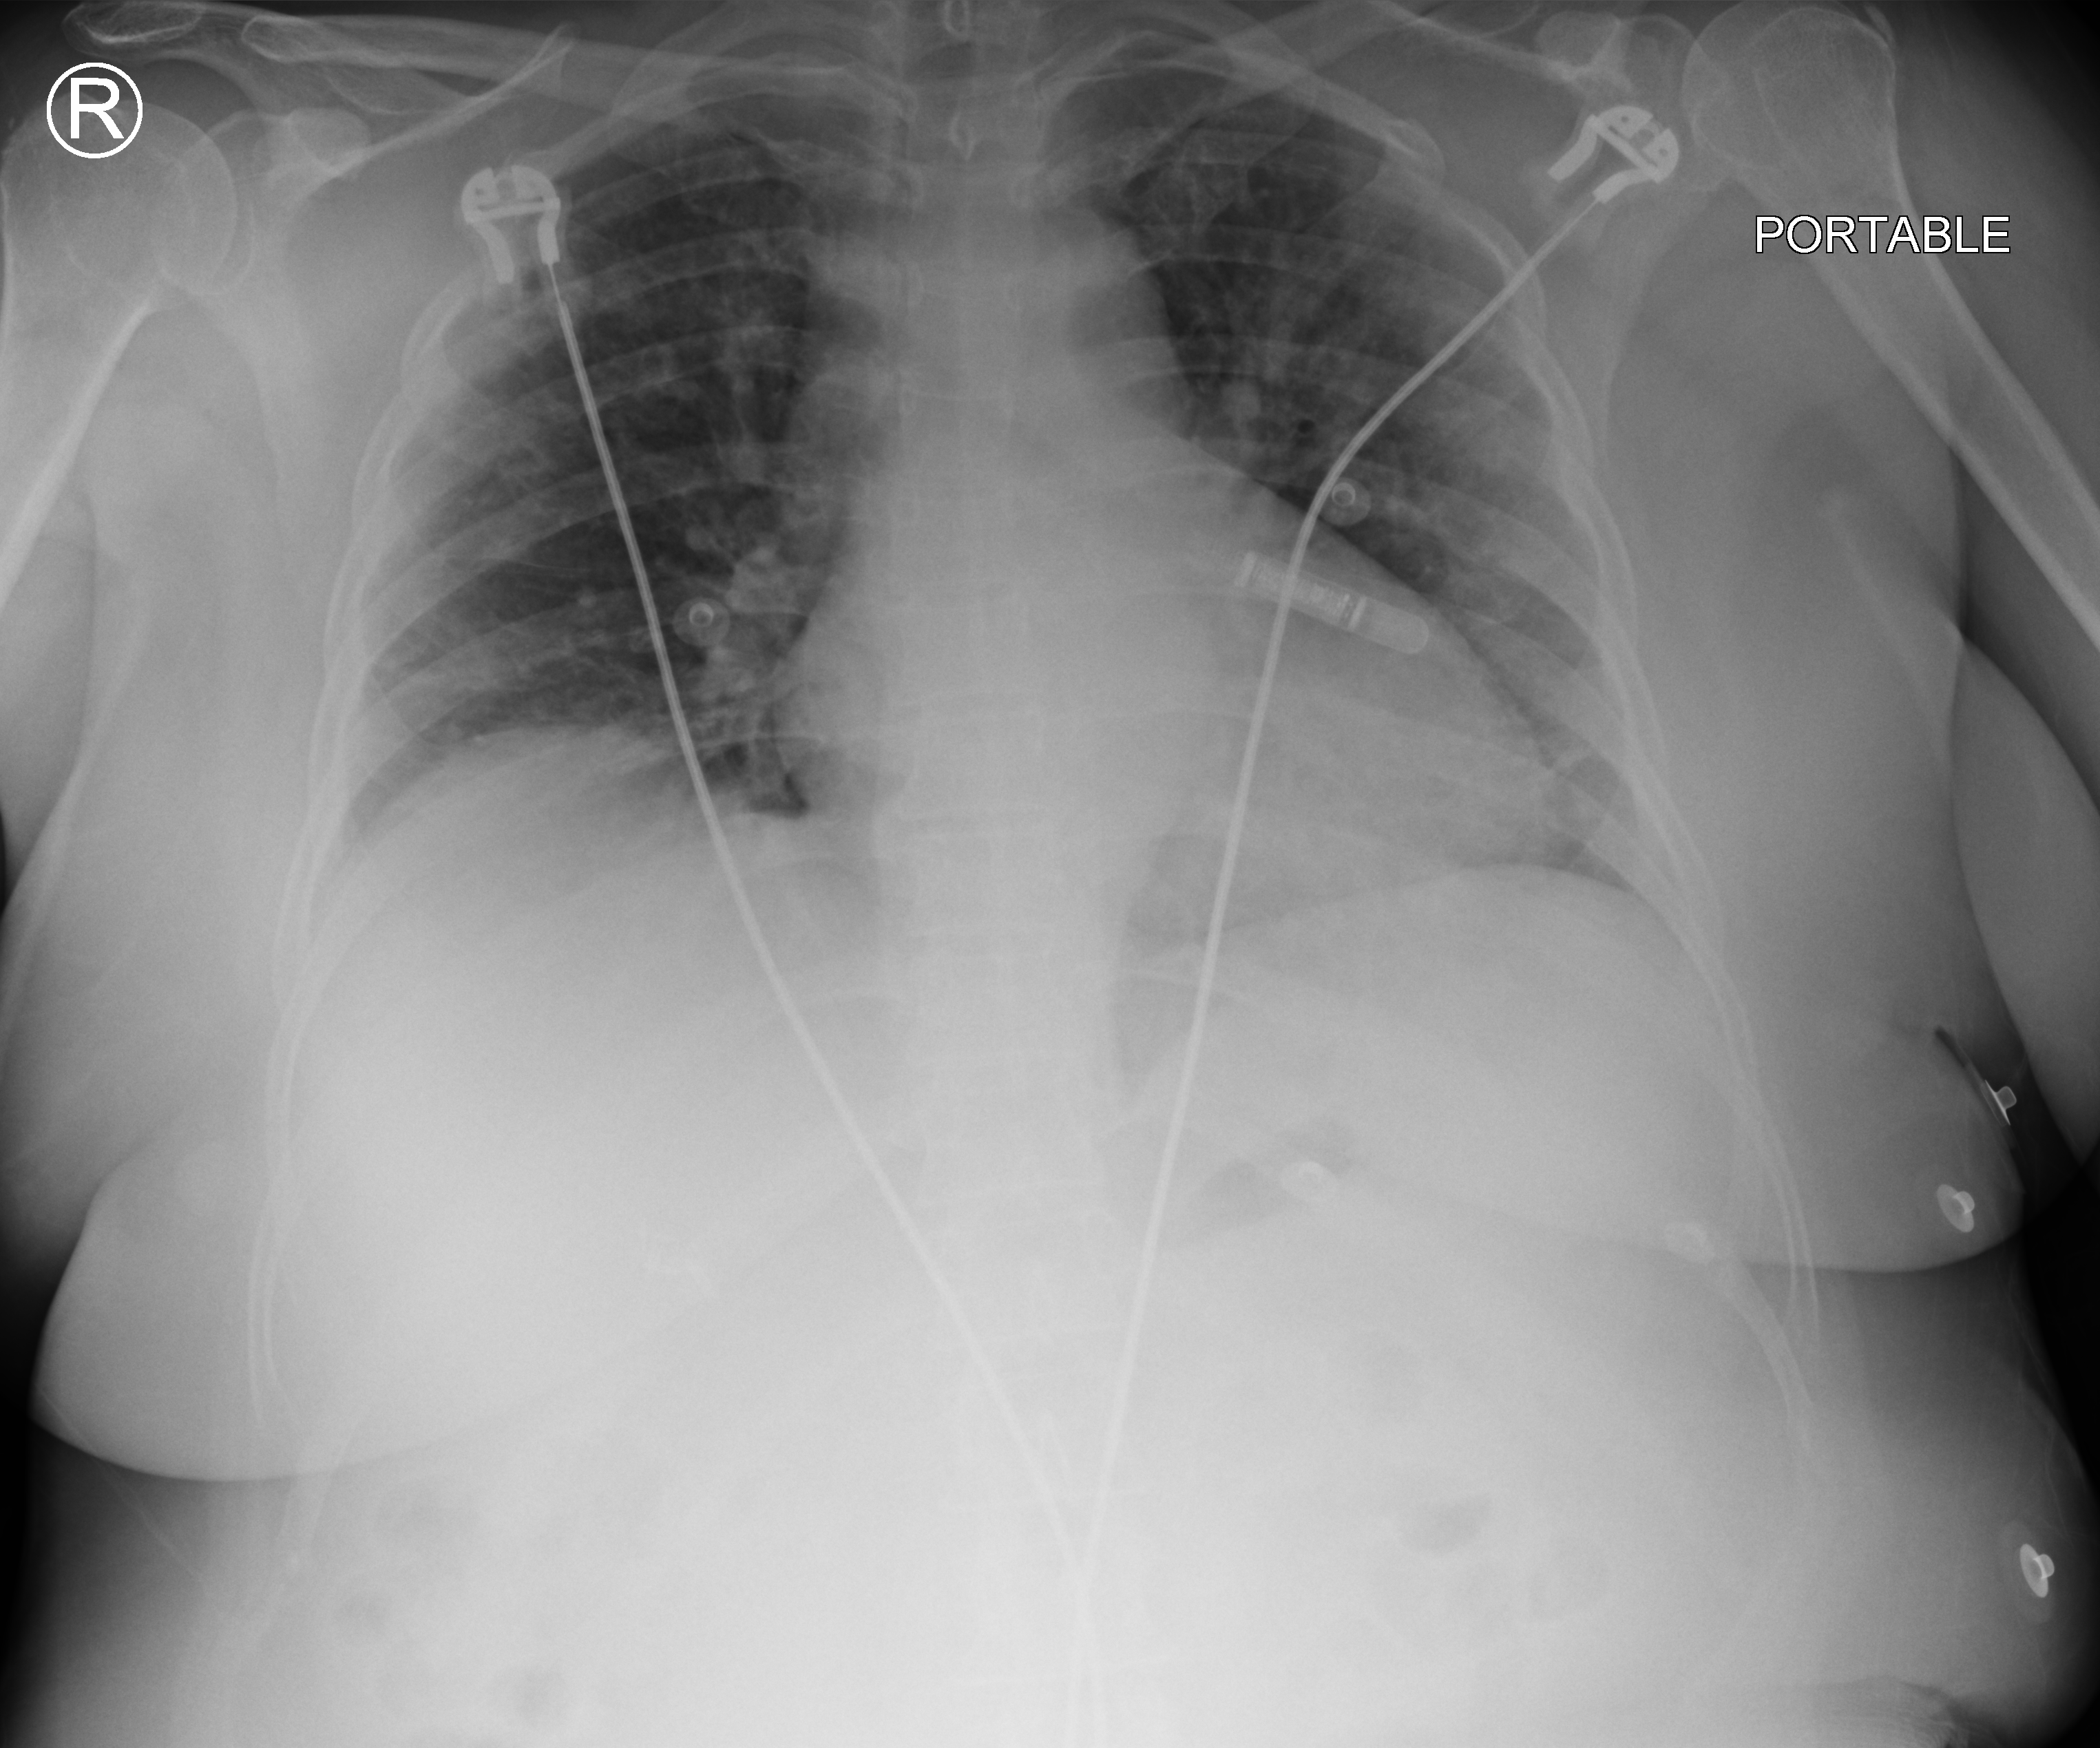
Bedside chest radiograph (computed radiography); anteroposterior (AP) projection. Patient hospitalised with COVID-19; female, aged 18–59 years.
From the hospital-stay record, not from the radiograph (when in the stay this image was taken is not recorded): other chronic lung disease (admission record): no; admitted to intensive care during this hospital stay: no; COPD (admission record): no.